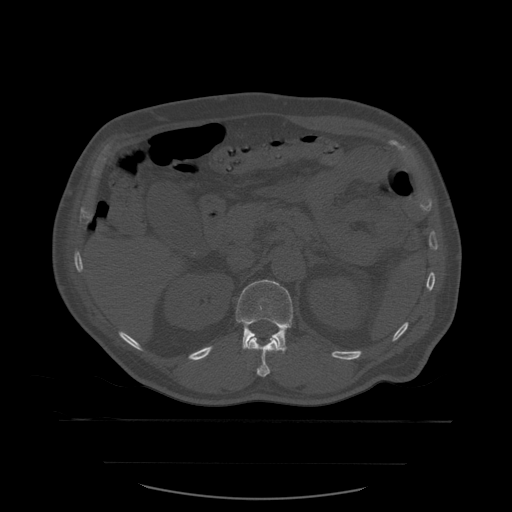
CT including the spine, one axial slice; slice 257 of 590 in the series (ordered by position); bone window (W 1800 / L 400 HU); 1.25 mm slice thickness; 512 × 512 image matrix. Patient age 71 years. Case-level facts recorded for this patient, not image findings: primary cancer: lung; vertebrae with lytic lesions (as recorded): T1, T2, L5, S1.
Structures marked on this image (semi-automatic segmentation, software-assisted and operator-edited):
- L1 vertebra: box from (x=236, y=280) to (x=293, y=354) px
- T12 vertebra: (x=242, y=334)–(x=283, y=377)